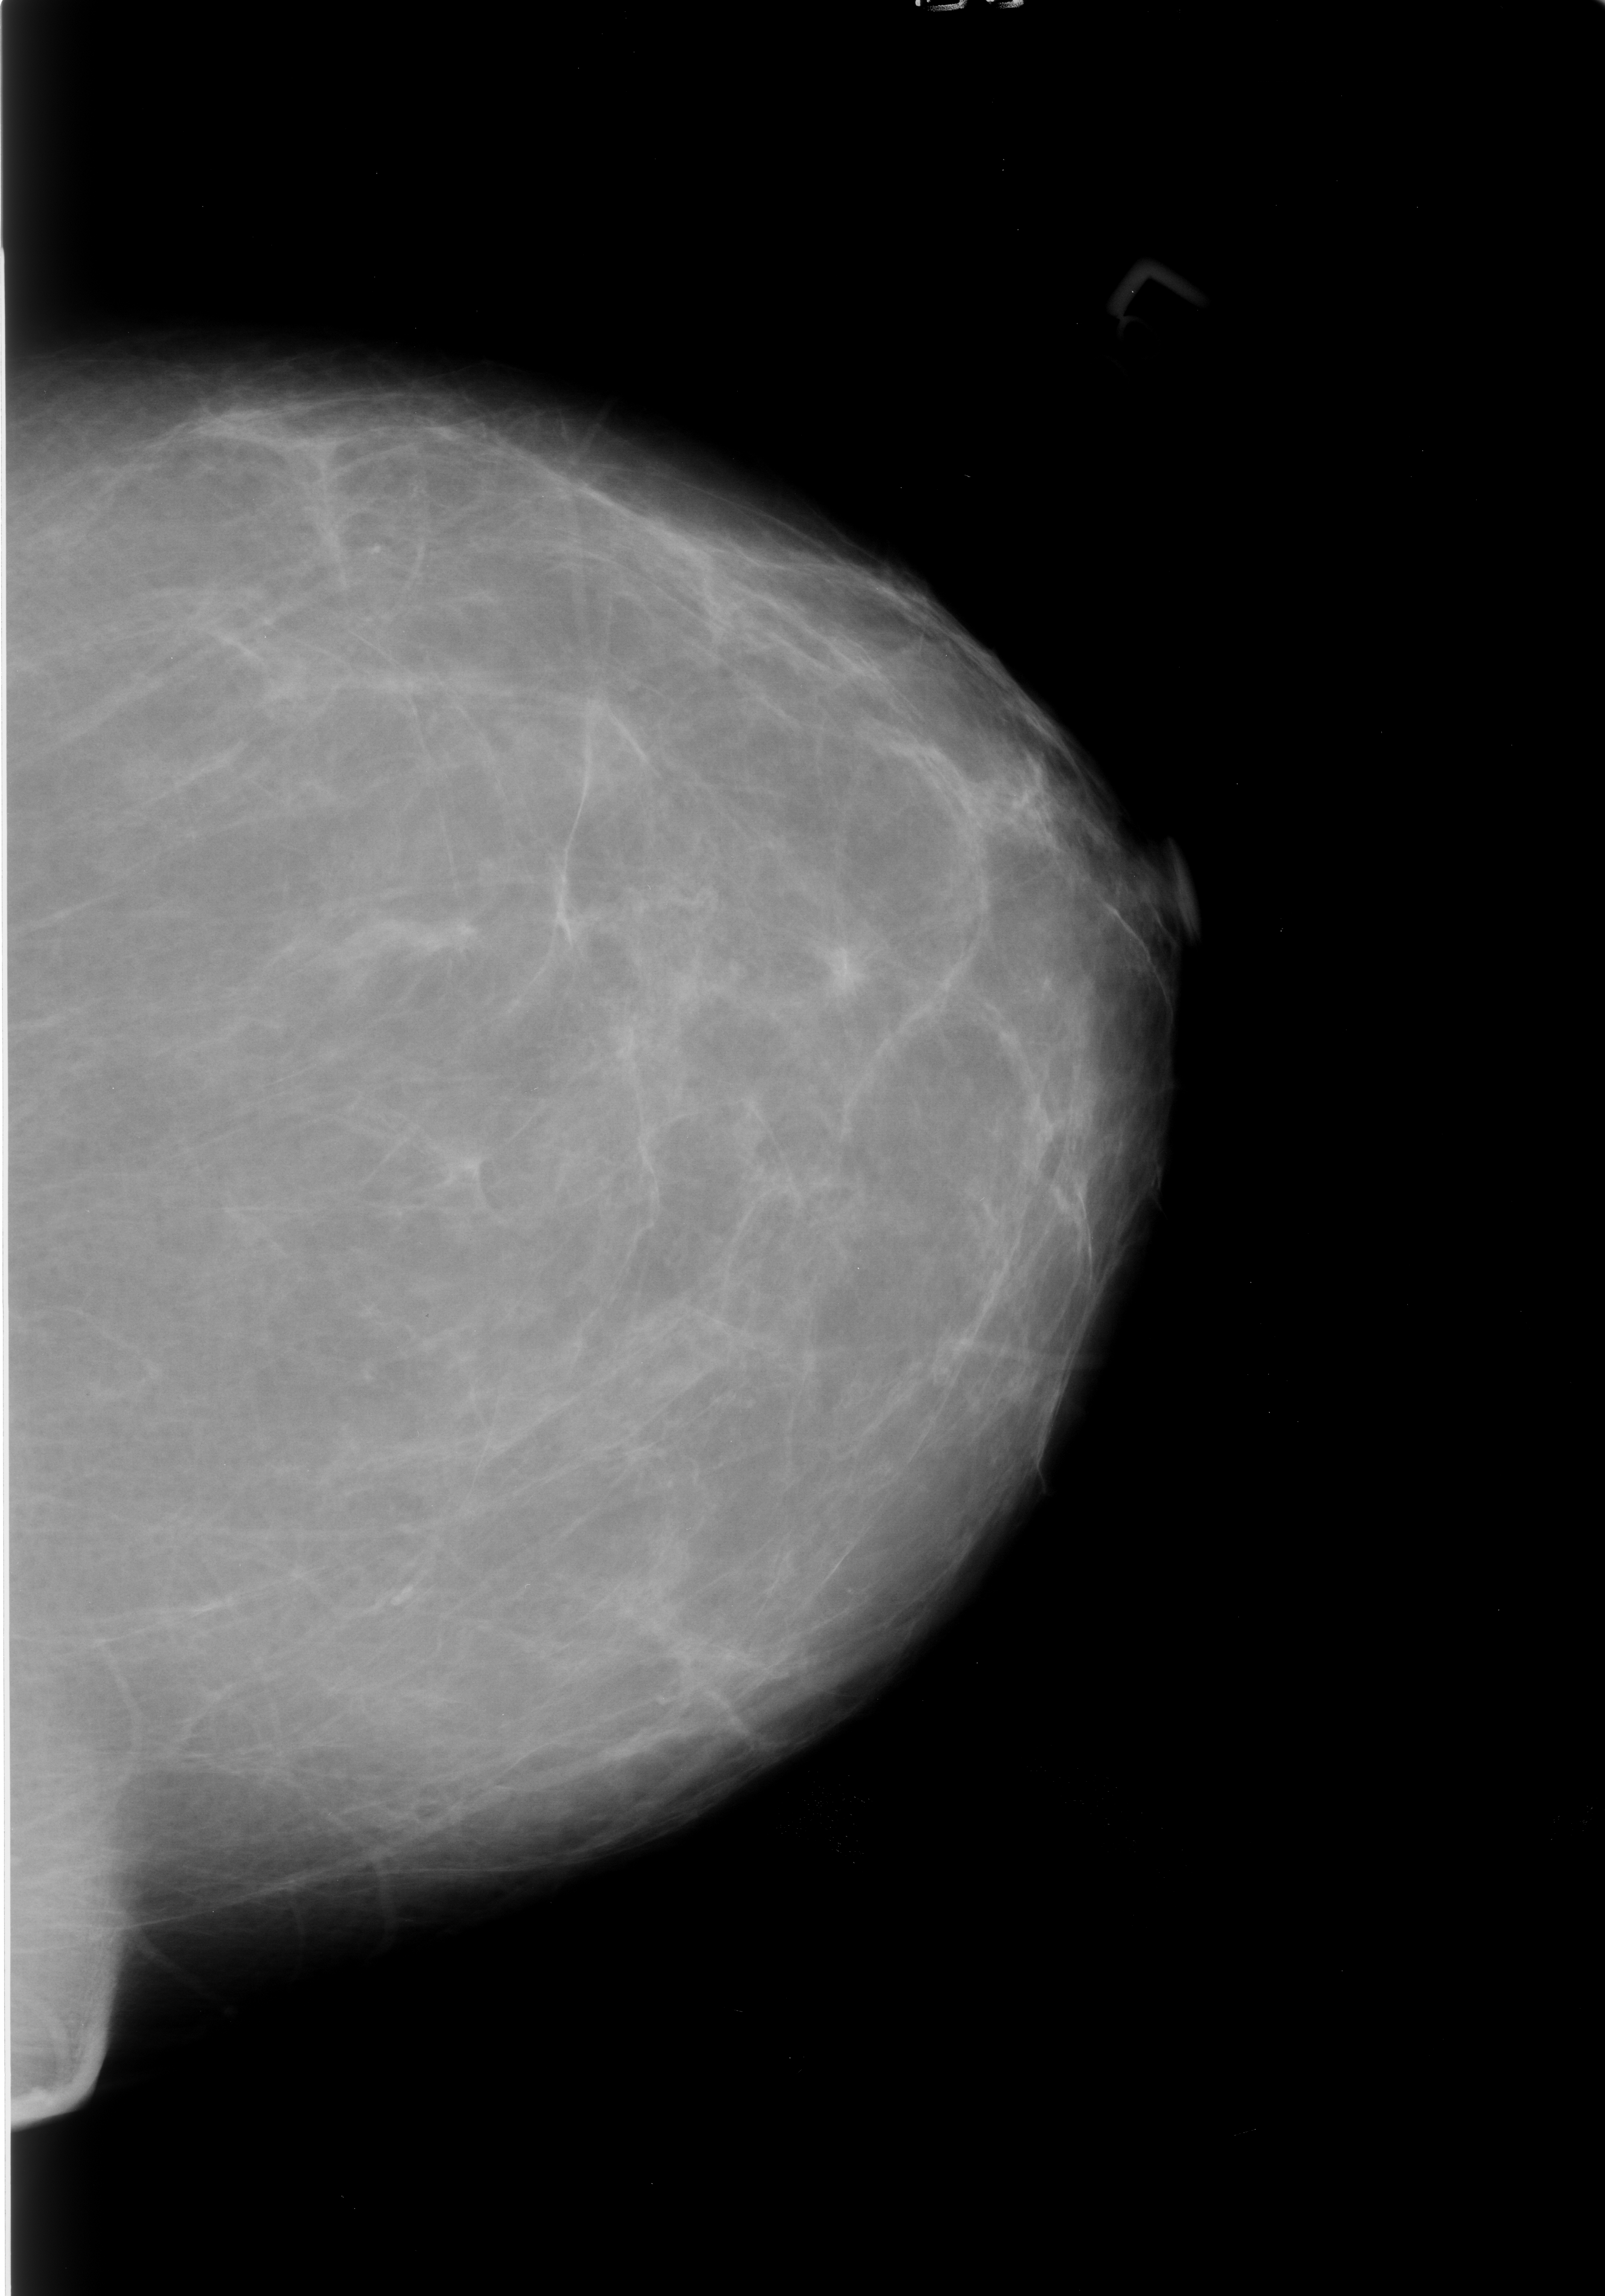
Scanned film-screen mammogram; left breast; craniocaudal (CC) view; BI-RADS breast density category 1 (scale 1–4).
Mass, shape irregular / architectural distortion, margins spiculated; BI-RADS assessment category 4; pathology (as recorded): malignant.